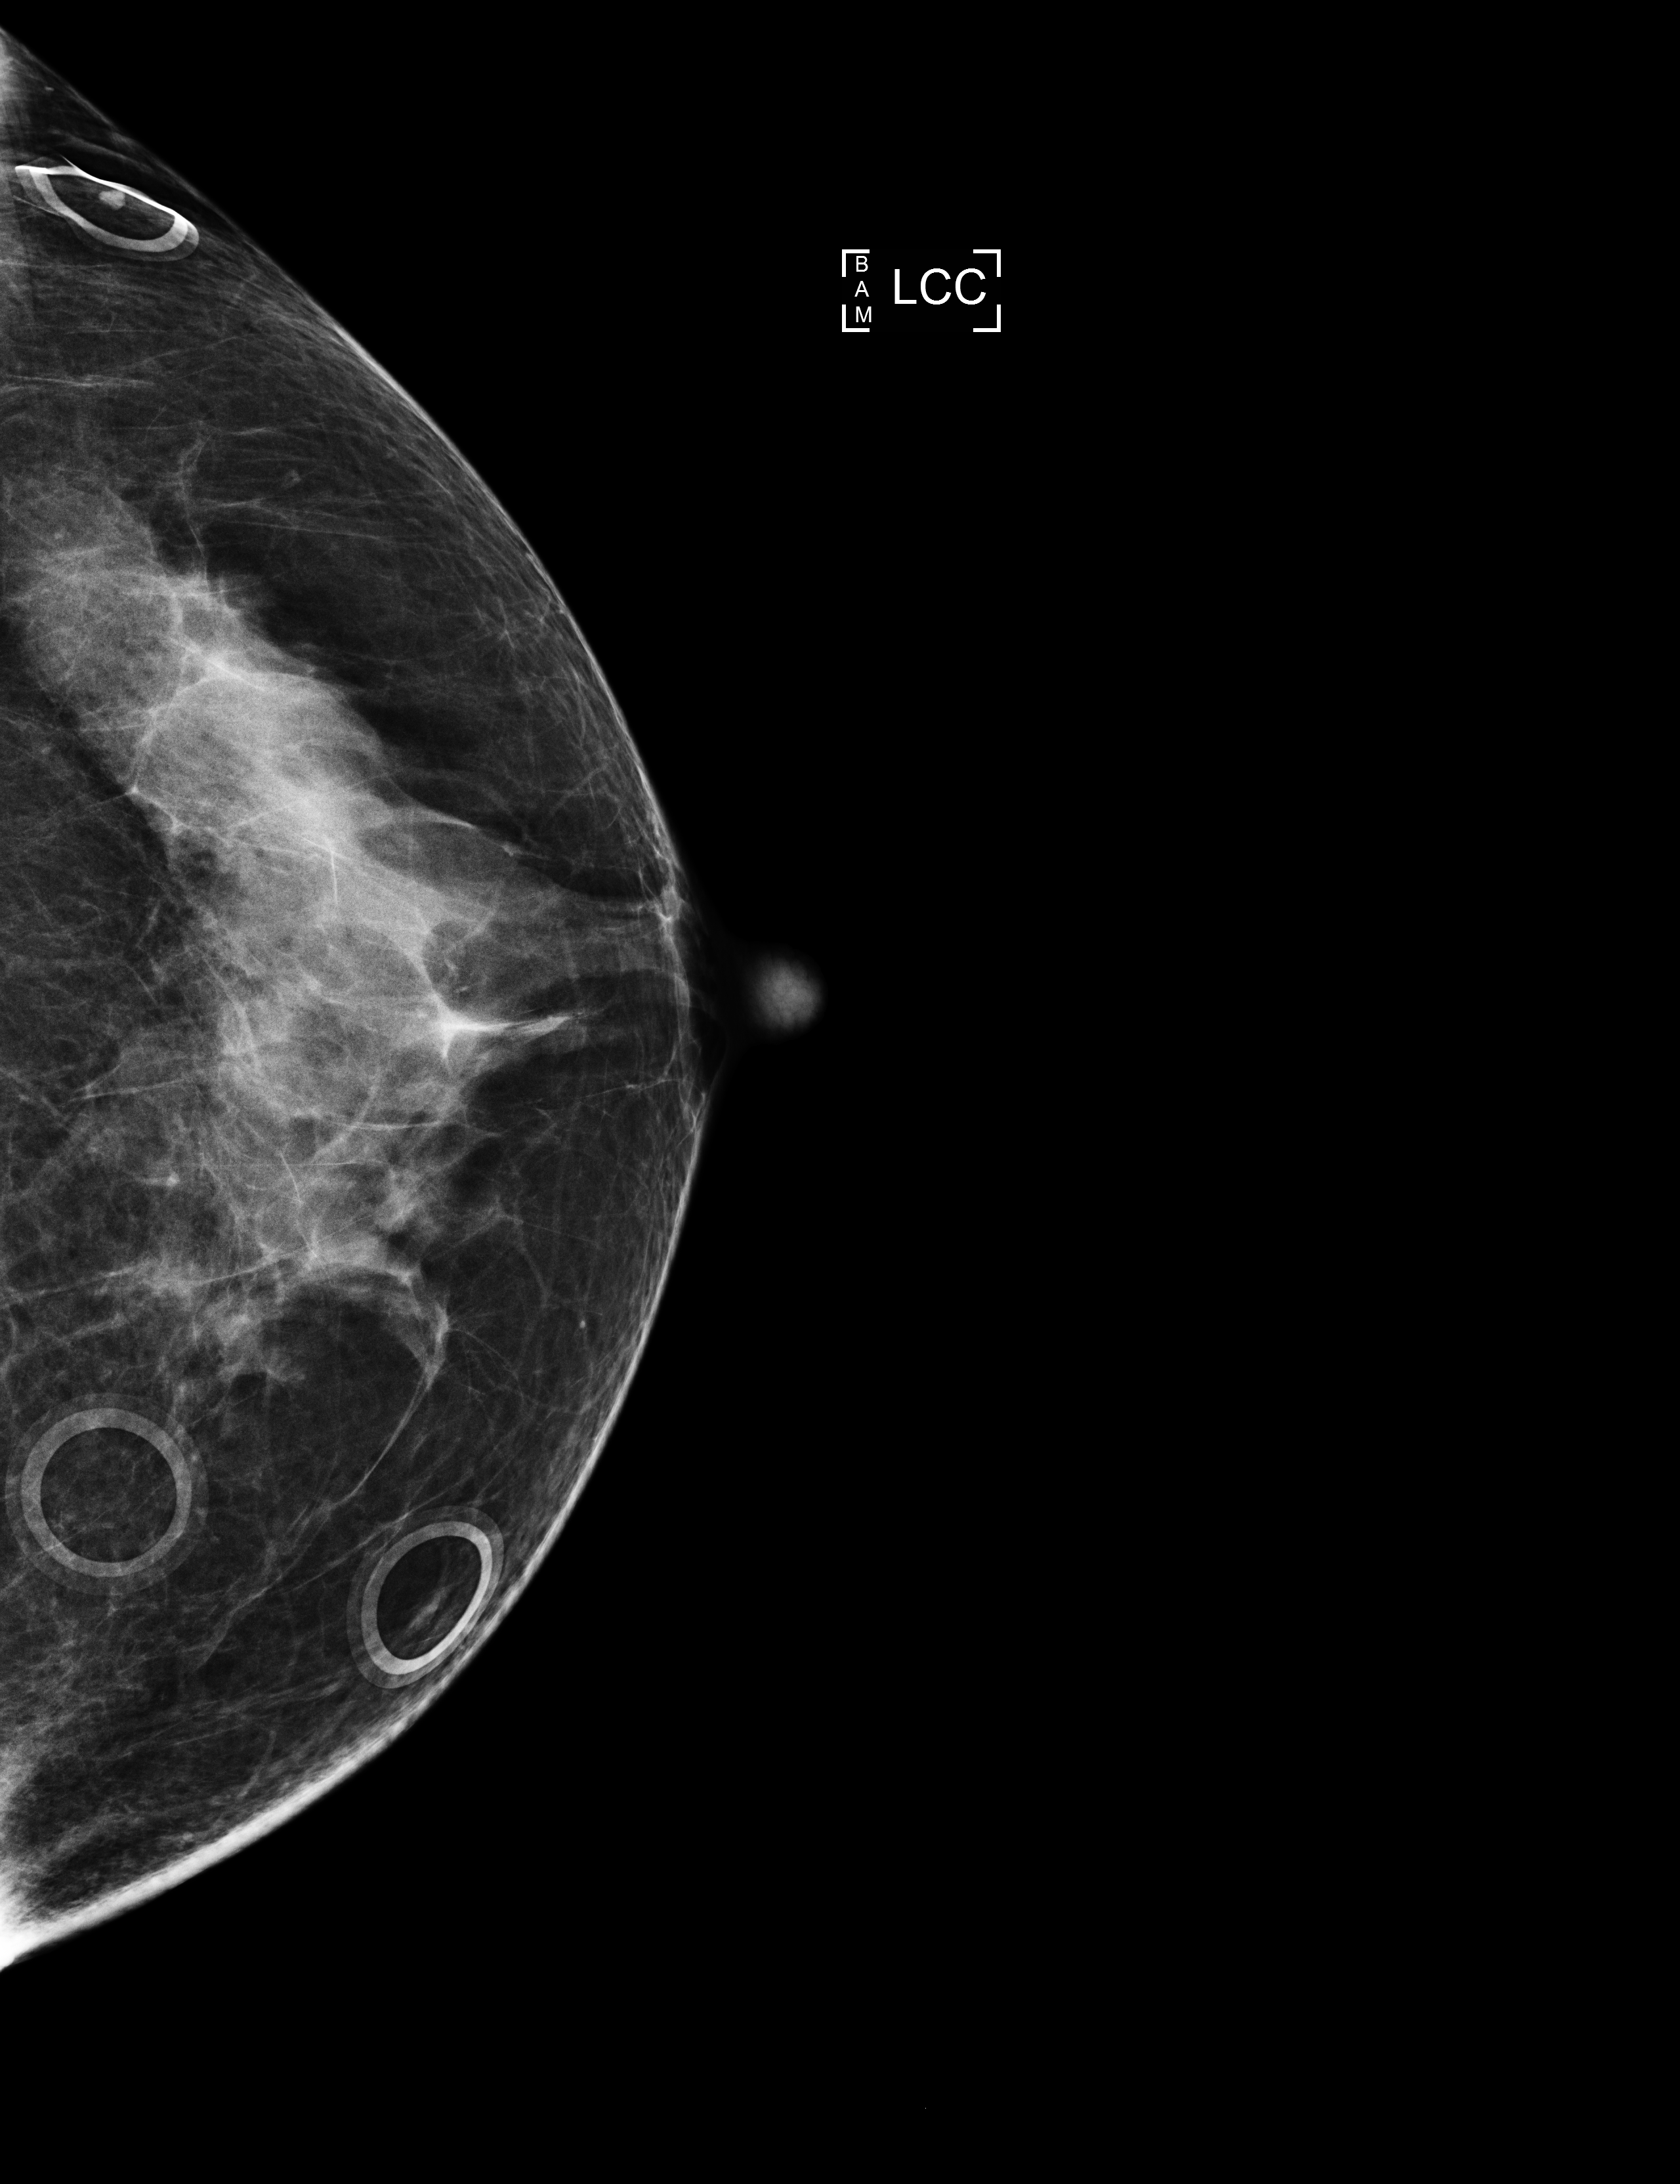
Screening examination, system: Selenia Dimensions. Female patient, age 60 years.
Image type: full-field digital mammogram. Breast: left. Projection: cranio-caudal projection.